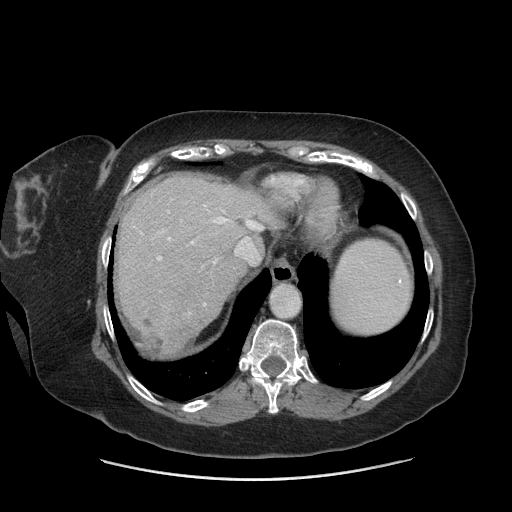
Contrast-enhanced abdominal CT (liver protocol), one axial slice. Position 59 of 69 along the scan axis. Reconstruction kernel STANDARD. 140 kVp. Soft-tissue window (W 400 / L 40 HU). 2.5 mm slice thickness. 512 × 512 image matrix, field of view 420 × 420 mm. Case-level facts recorded for this patient, not image findings: diagnosis: hepatocellular carcinoma (patient treated with transarterial chemoembolisation; whether this scan precedes or follows treatment is not stated here); TNM stage (as recorded): Stage-IIIB; Child-Pugh class: A; tumour differentiation: moderately differentiated.
Outlined on this slice (semi-automatically segmented with operator editing):
- abdominal aorta: bounding box (x1, y1, x2, y2) in pixels: (271, 284, 300, 317)
- liver parenchyma outside the tumour (the mass and vessels are separate outlines, so this box may not span the whole liver): (116, 174, 281, 352)
- mass: (140, 309, 186, 355)
- liver vessels: (157, 205, 263, 306)